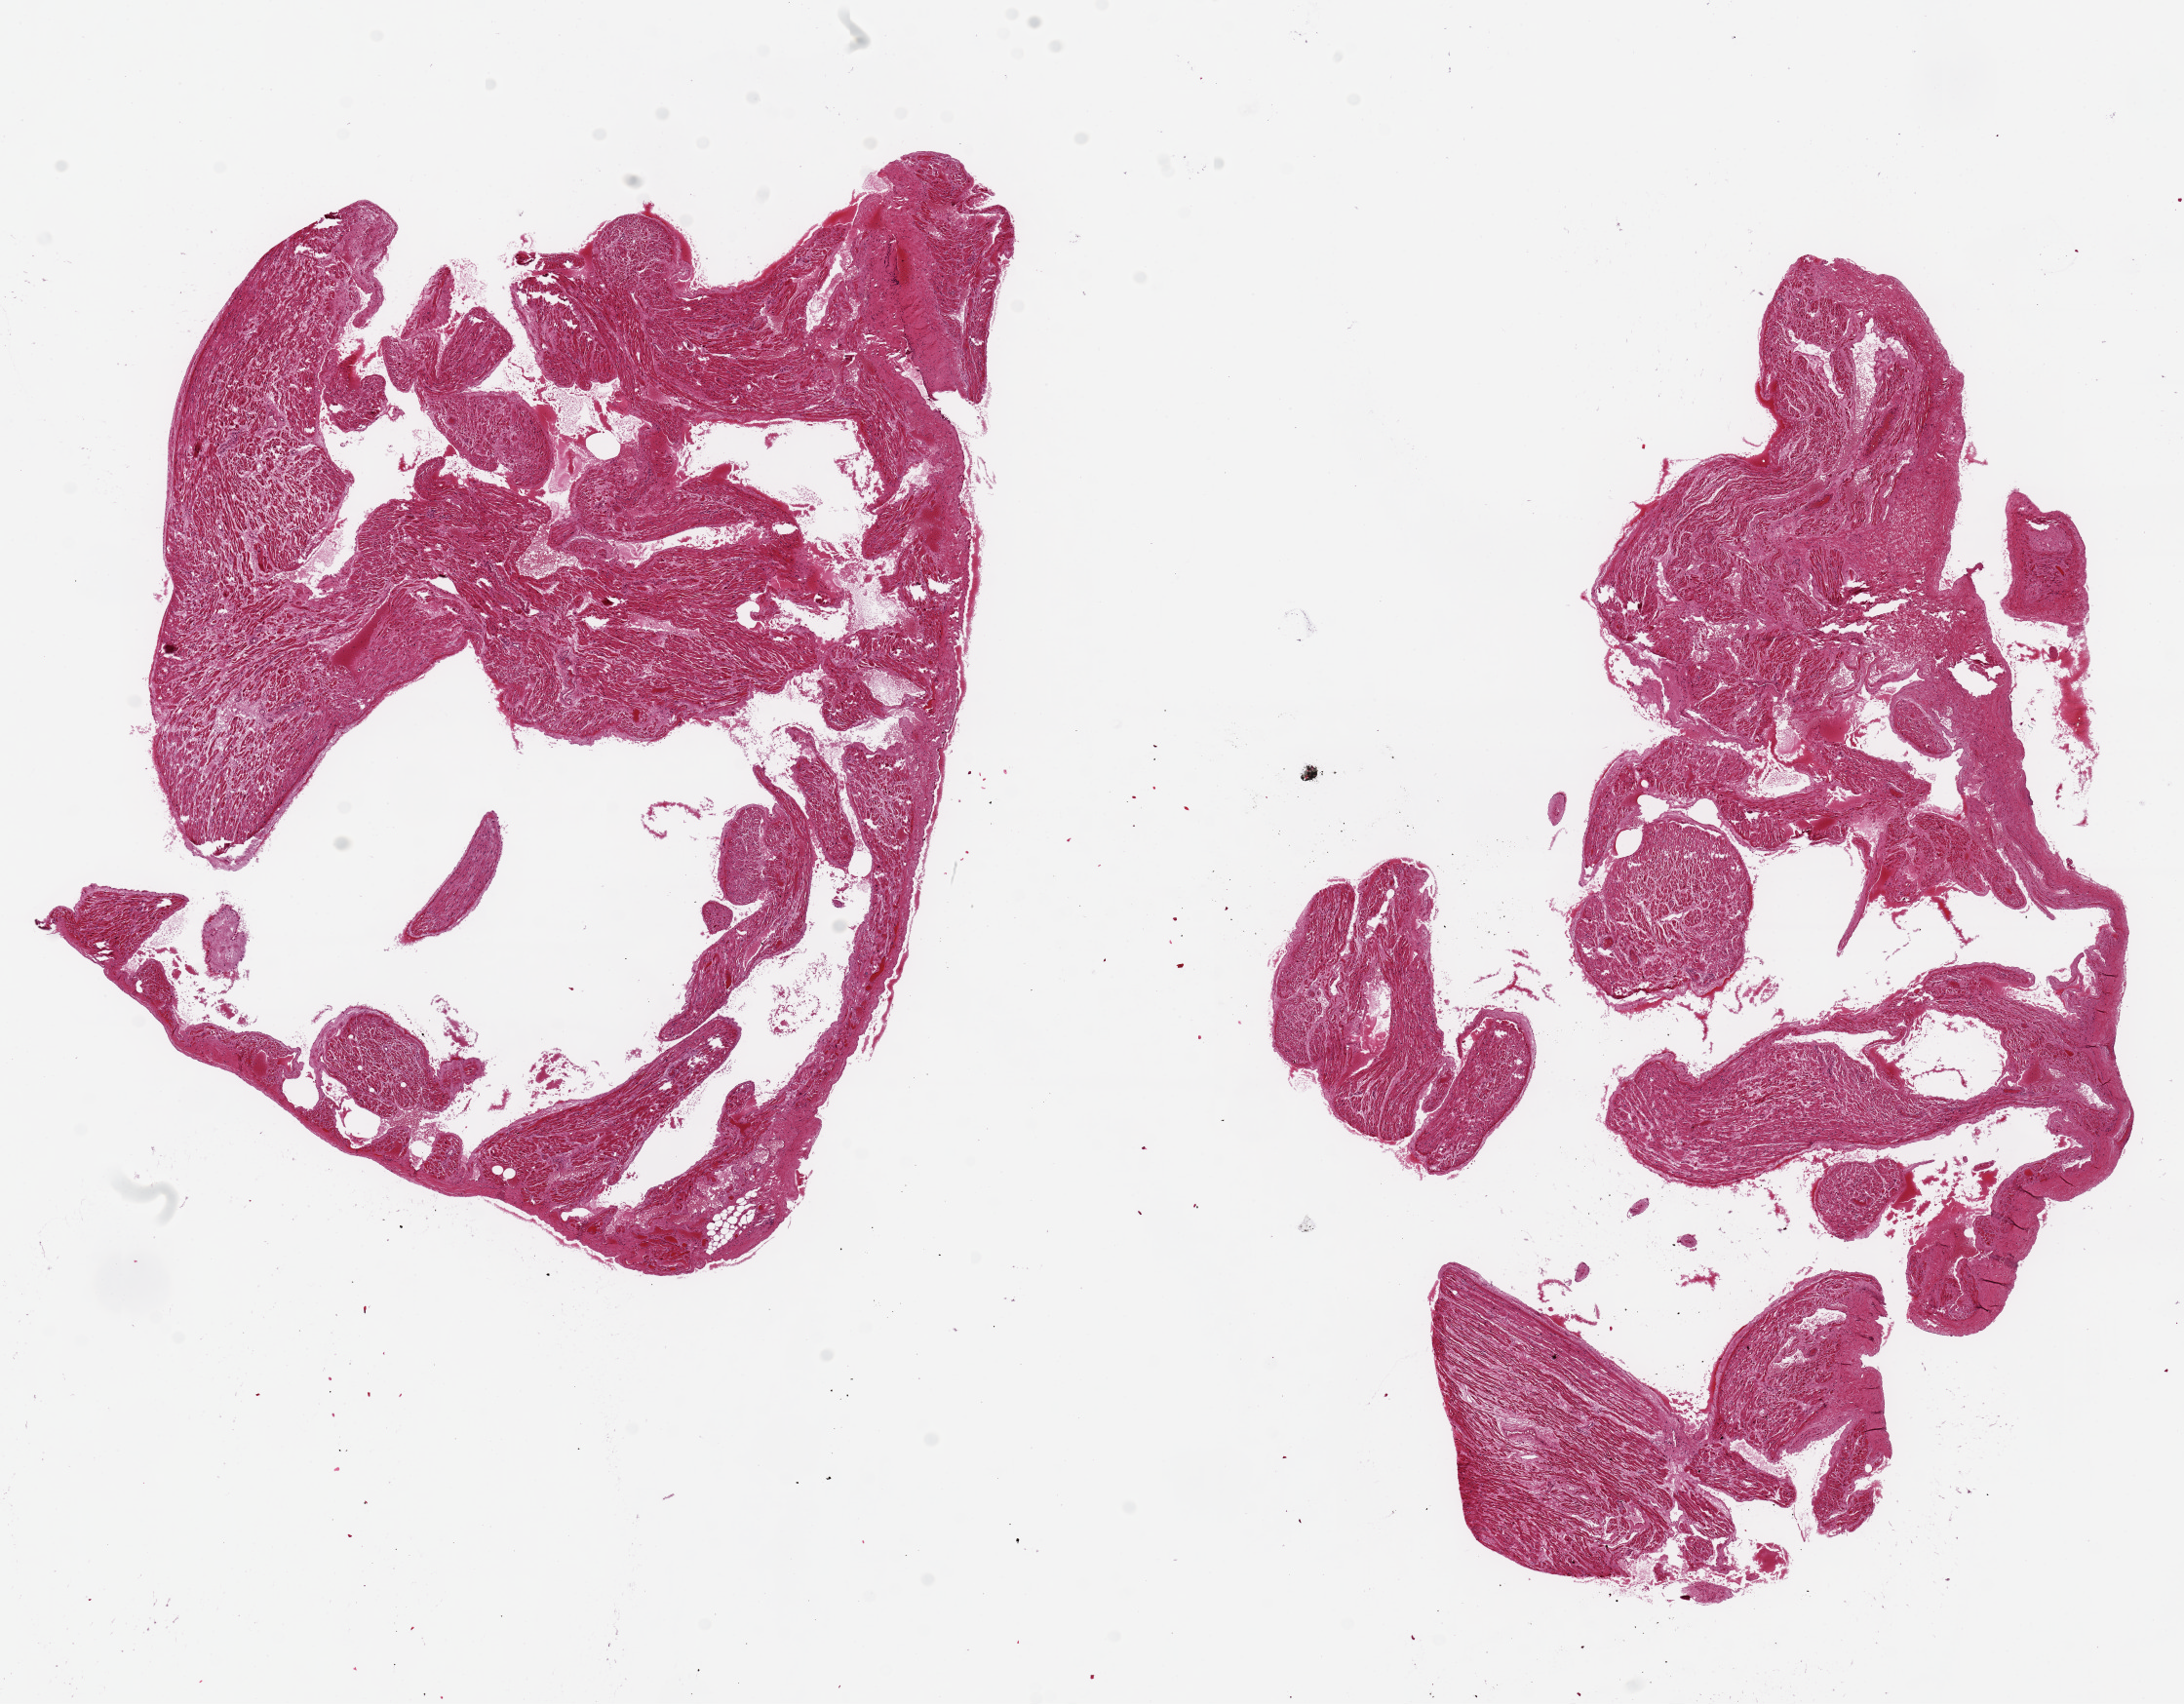
Digitized haematoxylin and eosin-stained section, brightfield — whole scanned area (about 17.7 x 13.8 mm) shown as a low-resolution overview, PAXgene-fixed, paraffin-embedded tissue, target tissue: auricular appendage, donor tissue sample. Donor: male.
* review note (as recorded): 2 pieces ~10x4mm, unusally badly autolyzed